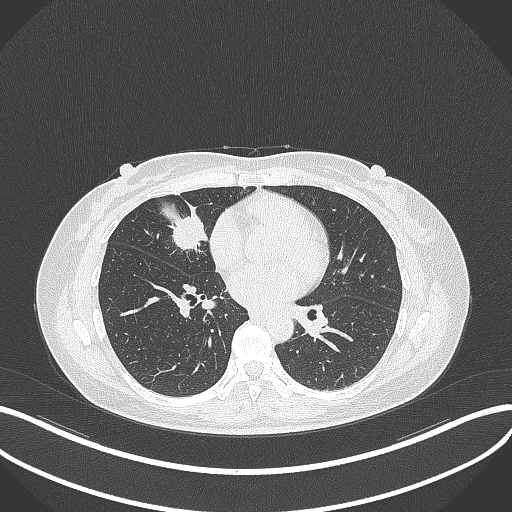
Chest CT, one axial slice. Slice 133 of 284 in the series (ordered by position). Reconstruction kernel B70f. 120 kVp. Lung window (W 1500 / L -600 HU). 512 × 512 image matrix, field of view 400 × 400 mm. Female patient, age 43 years. Case-level facts recorded for this patient, not image findings: clinical TNM (as recorded): T1c N3 M1.
Outlined on this slice (bounding box drawn by a radiologist):
- lung tumour (recorded histology: adenocarcinoma): bounding box <166,207,208,253> (left, top, right, bottom; pixels)